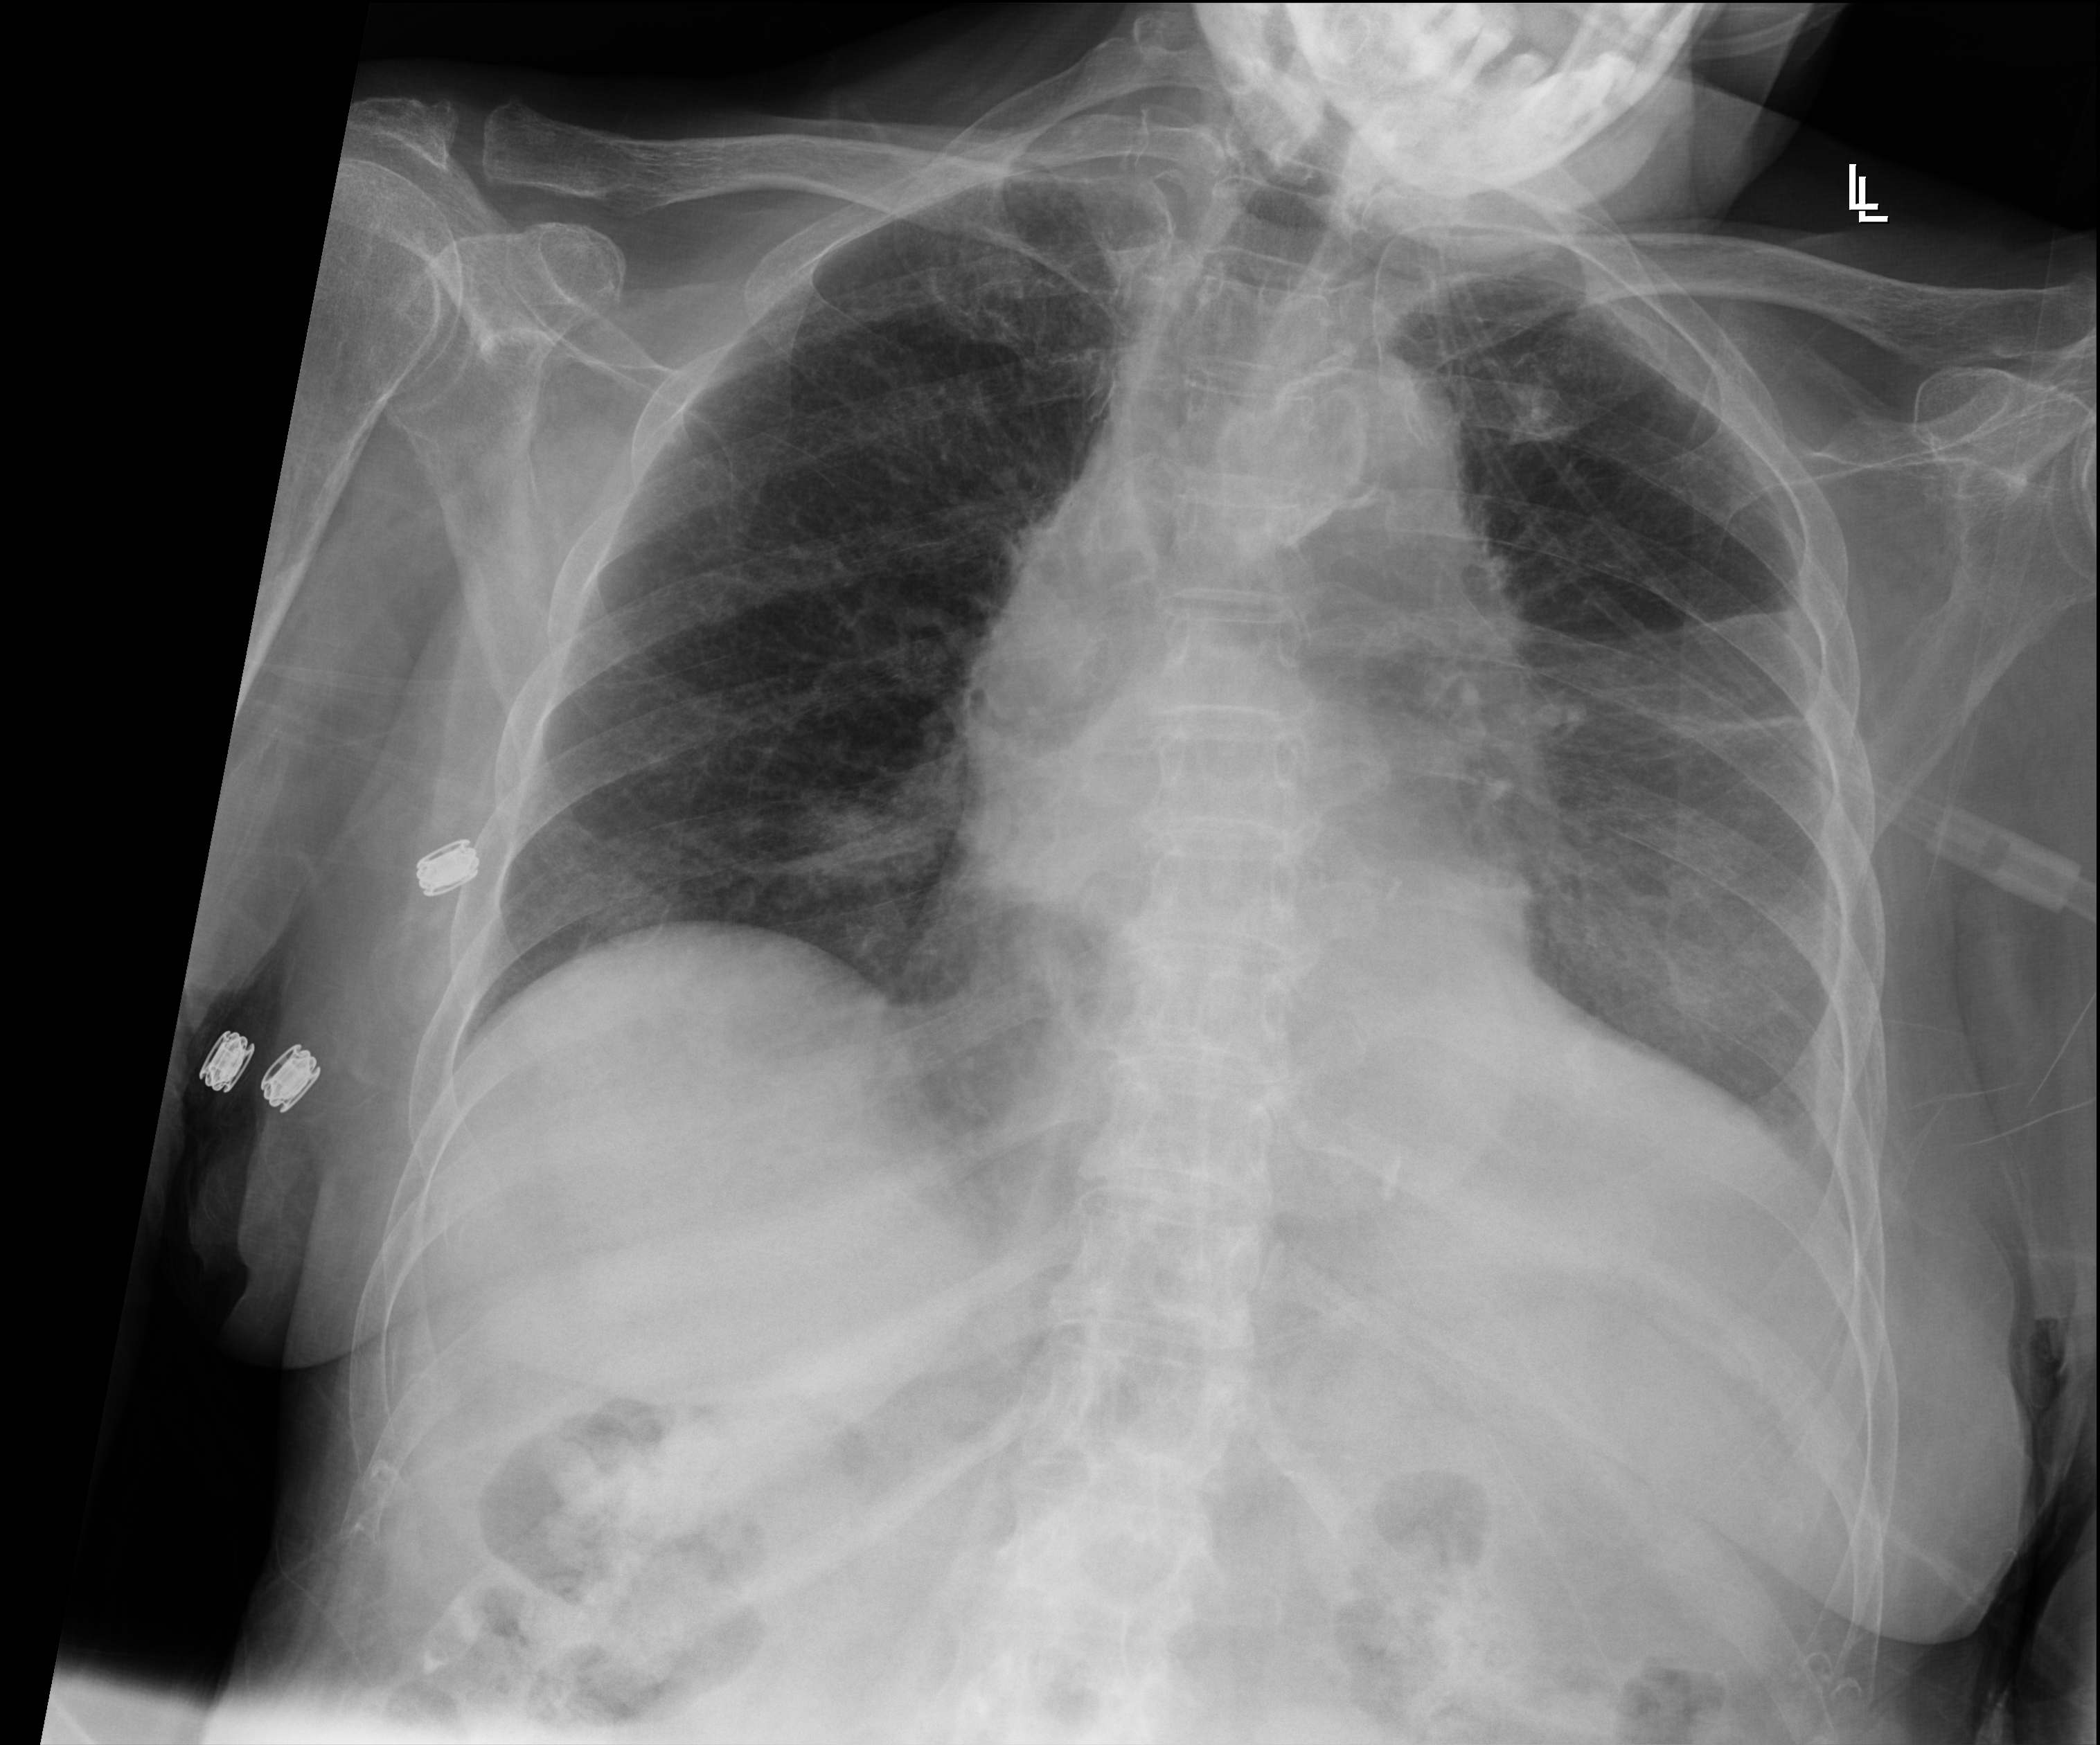
Chest radiograph (digital radiography); anteroposterior (AP) projection. Patient hospitalised with COVID-19; female, aged 75–90 years.
Hospital-stay facts (about this admission, not read from this image; timing relative to this image not recorded):
- mechanically ventilated during this hospital stay: no